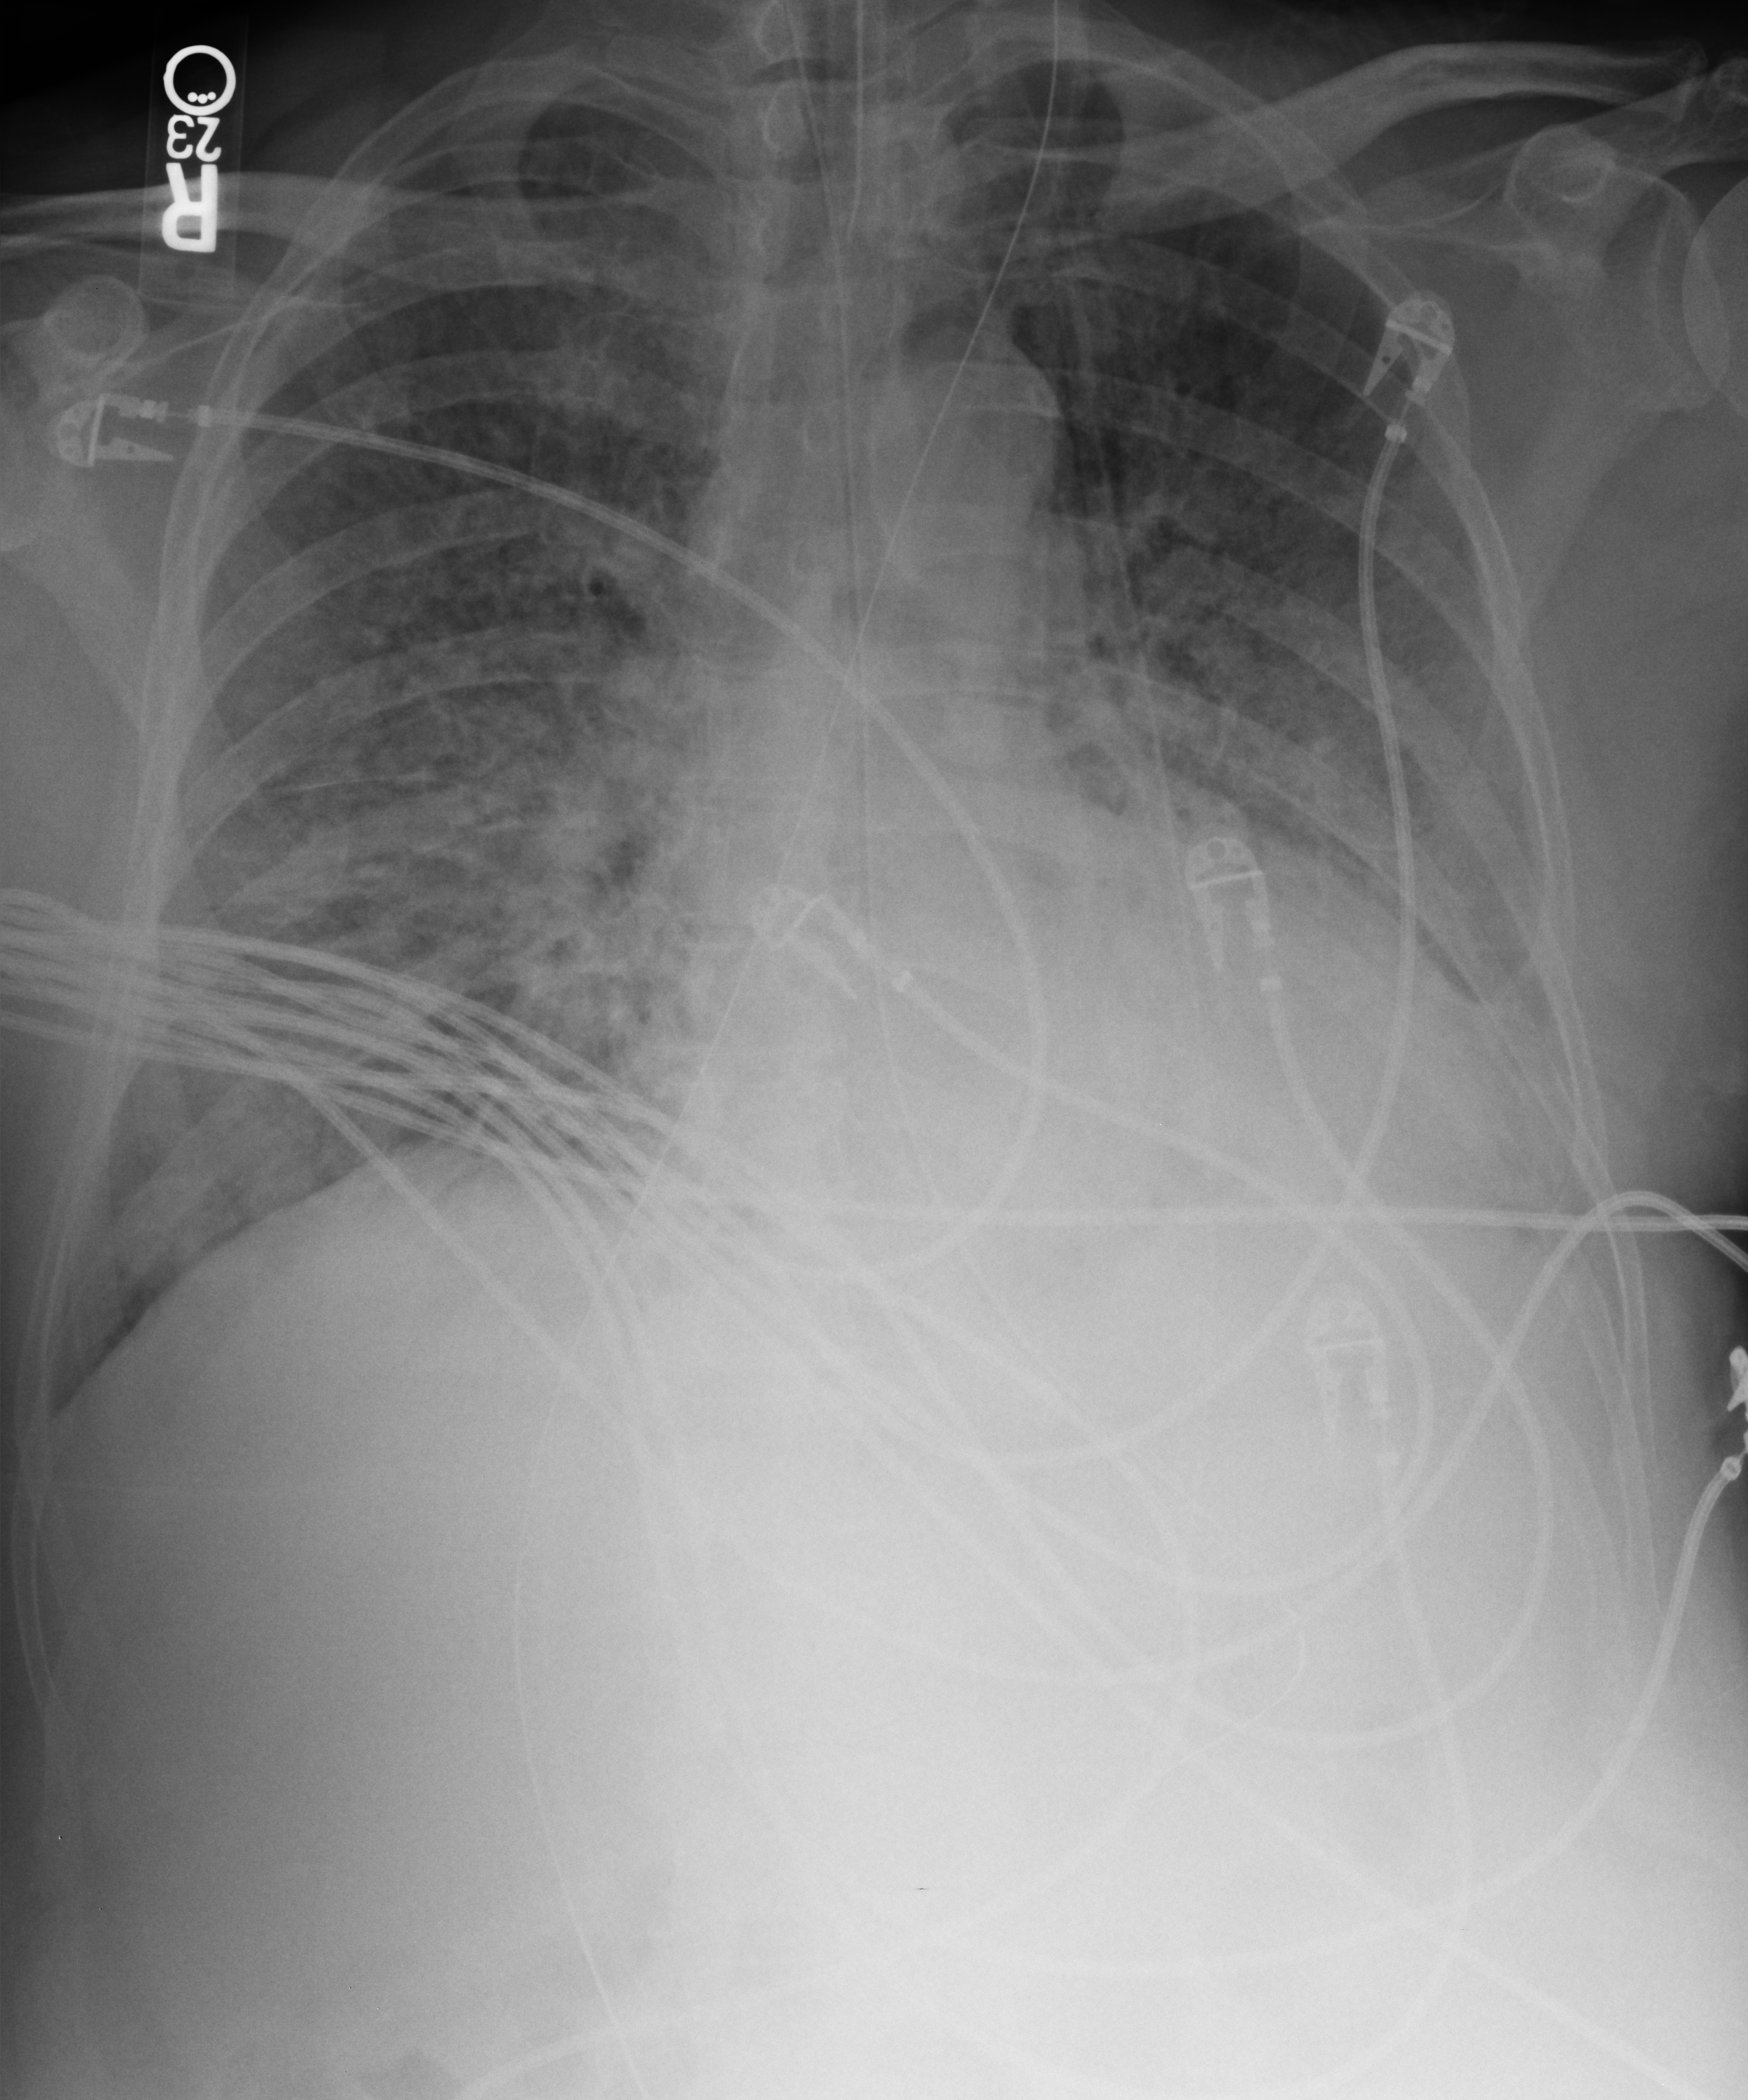
Bedside chest radiograph (computed radiography); anteroposterior (AP) projection. Male patient hospitalised with COVID-19, age 60–74 years.
Hospital-stay facts (about this admission, not read from this image; timing relative to this image not recorded):
- length of hospital stay: 28 days
- admitted to intensive care during this hospital stay: yes
- mechanically ventilated during this hospital stay: yes